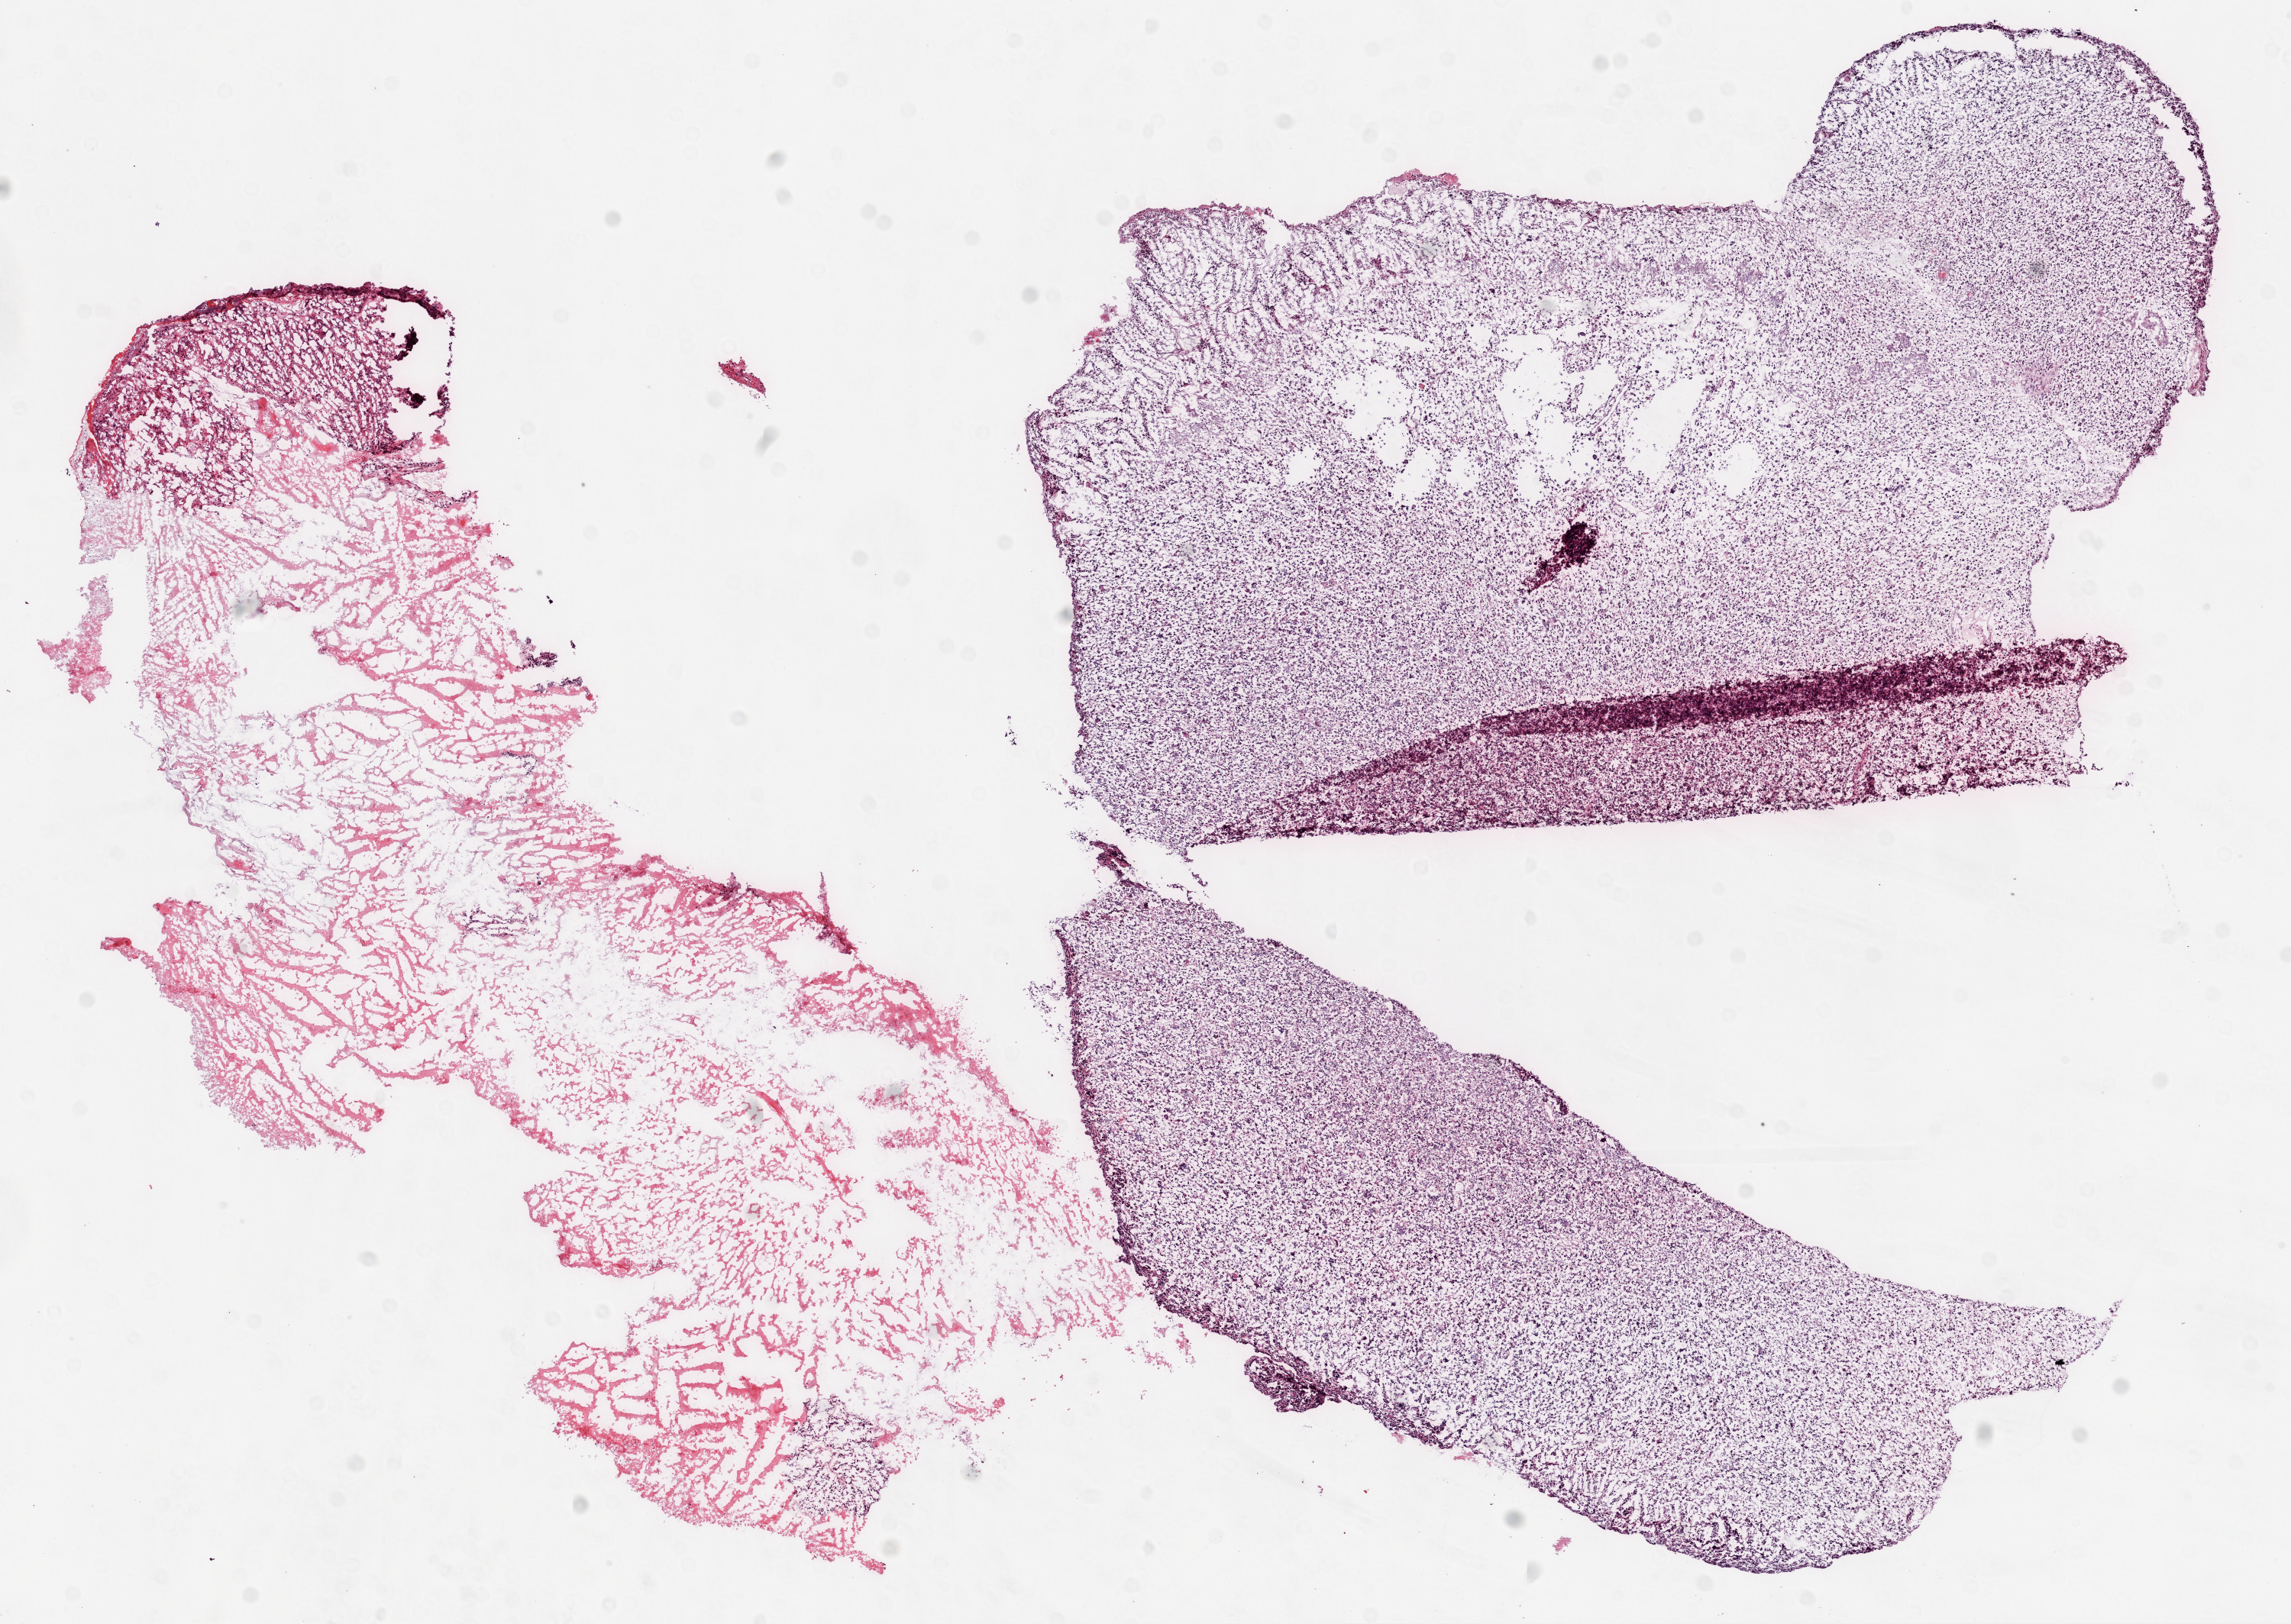
Whole-slide histology image, Hematoxylin and eosin (H&E) stained — a low-resolution overview of the entire scanned area, about 12.0 x 8.5 mm. Frozen section from the top of the tissue portion. Brain, primary tumour sample. Patient: male, age at initial diagnosis 69 years. Slide review estimates, as recorded: tumour cells 60%, tumour nuclei 100%, normal cells 0%, stromal cells 0%, necrosis 40%.
Pathologic diagnosis: Glioblastoma.